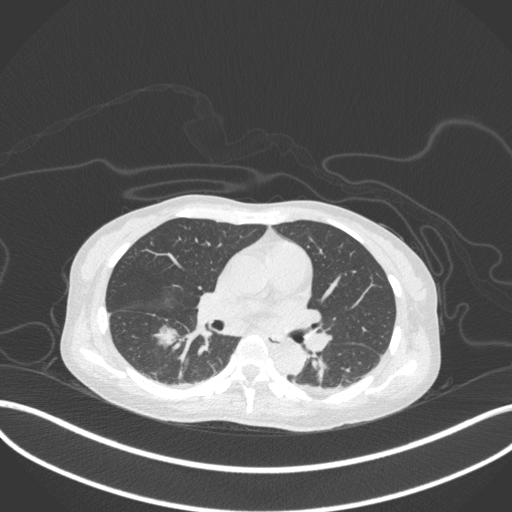
Chest CT, one axial slice; slice 166 of 260 in the series (ordered by position); 120 kVp; lung window (W 1500 / L -600 HU); 1 mm slice thickness; 512 × 512 image matrix, field of view 400 × 400 mm. Female patient, age 44 years. Case-level facts recorded for this patient, not image findings: clinical TNM (as recorded): T1c N0 M0.
Structures marked on this image (bounding box drawn by a radiologist):
- lung tumour (recorded histology: adenocarcinoma): bounding box [x1, y1, x2, y2] px = [153, 318, 183, 357]